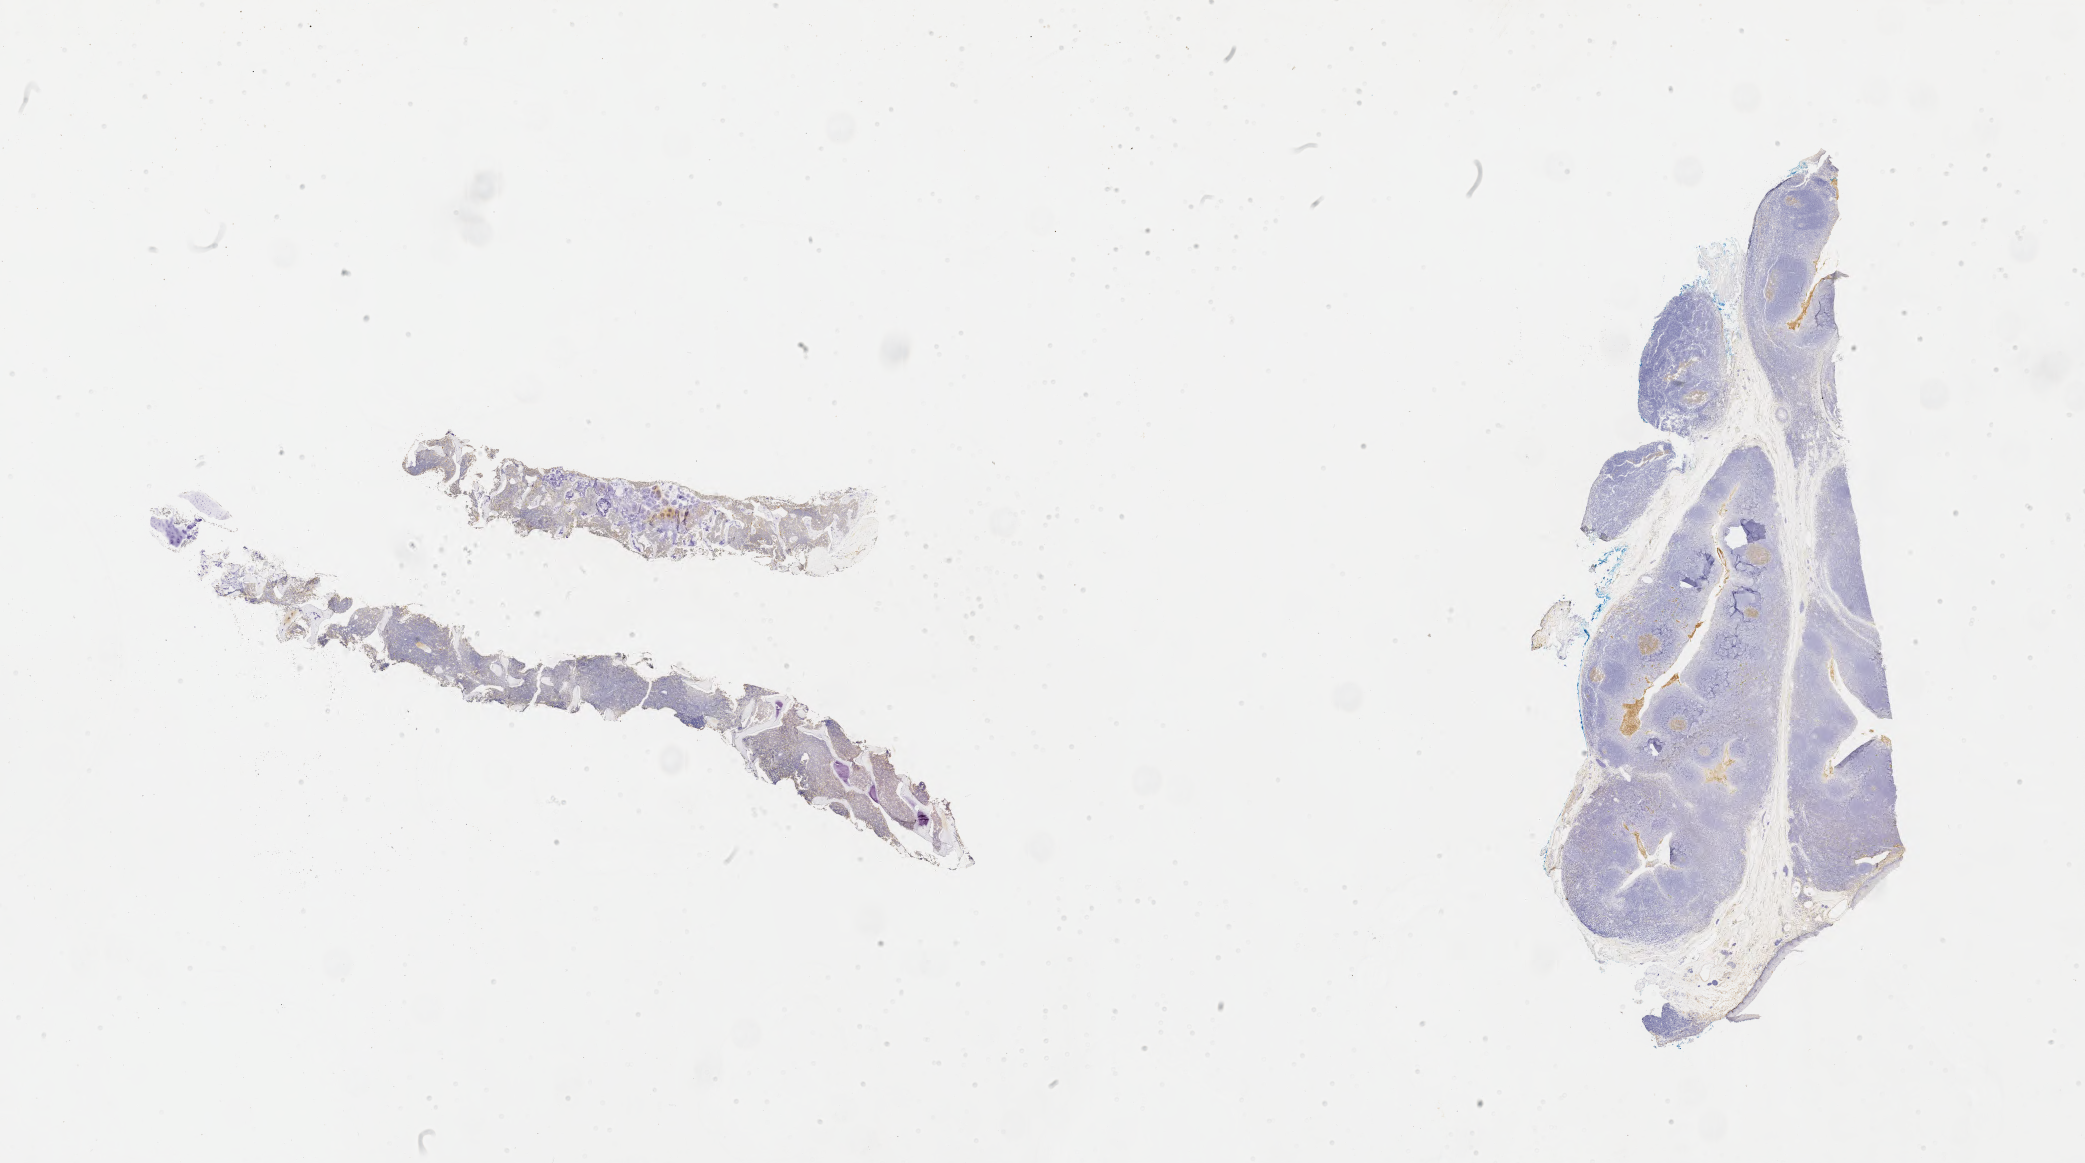
Immunohistochemistry (IHC) whole-slide image stained for CD10, whole scanned area (about 33.7 x 18.8 mm) shown as a low-resolution overview, tumor tissue, anatomic site: bone marrow. Male patient, 11 years old.
Histologic diagnosis: Burkitt lymphoma, NOS.